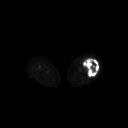
FDG PET of an extremity soft-tissue mass (from a PET/CT study), one axial slice; slice 213 of 267 in the series (ordered by position); 3.27 mm slice thickness; 128 × 128 image matrix, field of view 700 × 700 mm. Patient: female, 62 years. Case-level facts recorded for this patient, not image findings: histological type: undifferentiated – high grade; grade: high; site of the primary tumour: left thigh.
Outlined on this slice (expert contour drawn on MRI and transferred to this co-registered scan by the dataset authors):
- gross tumour volume including surrounding oedema: box from (x=82, y=58) to (x=99, y=77) px
- gross tumour volume (mass): (x=84, y=59)–(x=99, y=77)